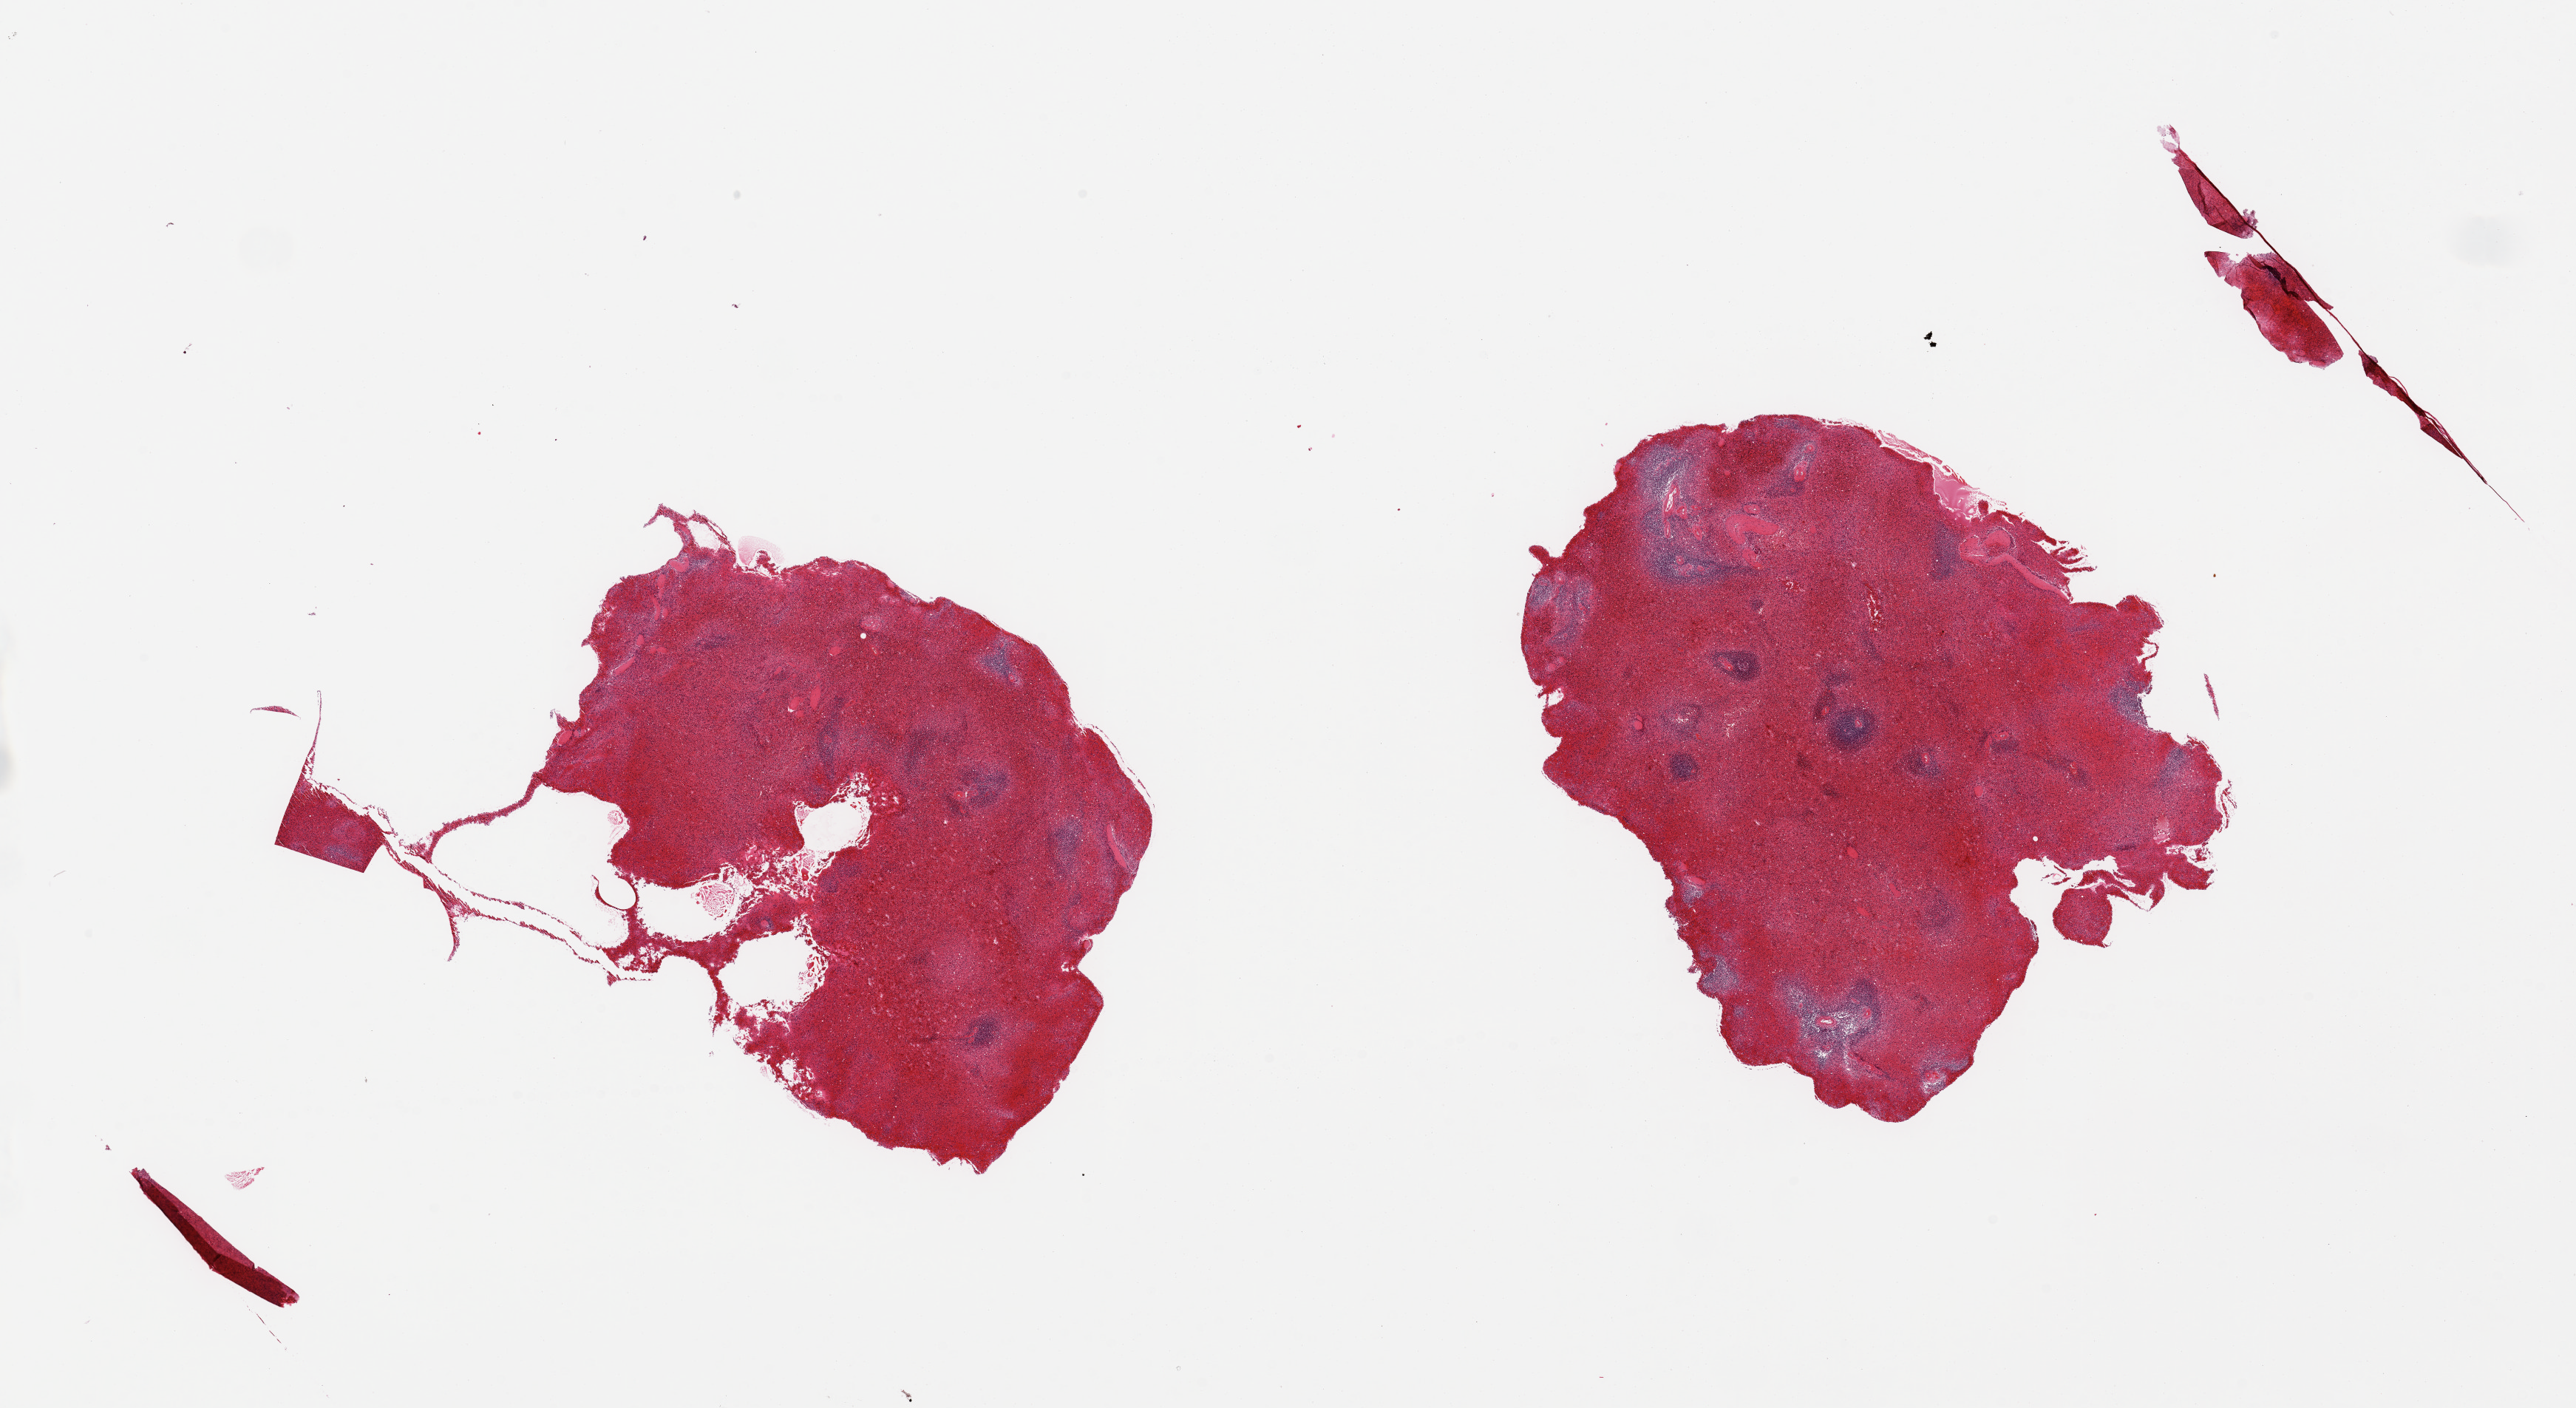
Digitized H&E-stained section — a low-resolution overview of the entire scanned area, about 27.6 x 15.1 mm (slide scanned at 20x), PAXgene-fixed paraffin-embedded (PFPE) section, section of spleen (target tissue), donor tissue sample. Donor: male.
Pathologist's review note for this sample: 2 pieces. severe congestion.